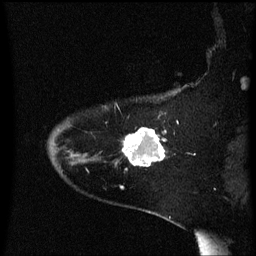
Breast MRI (dynamic contrast-enhanced), one sagittal slice. Dynamic contrast-enhanced series, image 2 of 3 at this slice position (ordered by acquisition). 1.5 T. TE 4.2 ms, TR 8.4 ms. 2 mm slice thickness. 256 × 256 image matrix. Patient: female, 54 years. Case-level facts recorded for this patient, not image findings: setting: breast cancer imaged before/during neoadjuvant chemotherapy; receptor status: HR-positive, HER2-negative.
Outlined on this slice (semi-automatically segmented with operator editing):
- analysis volume of interest (the breast-tissue region the enhancement analysis was run in; not a lesion): box from (x=118, y=128) to (x=166, y=167) px
- tumour enhancement mask (voxels above the 70 % enhancement threshold inside the analysis volume of interest): (x=123, y=128)–(x=166, y=167)